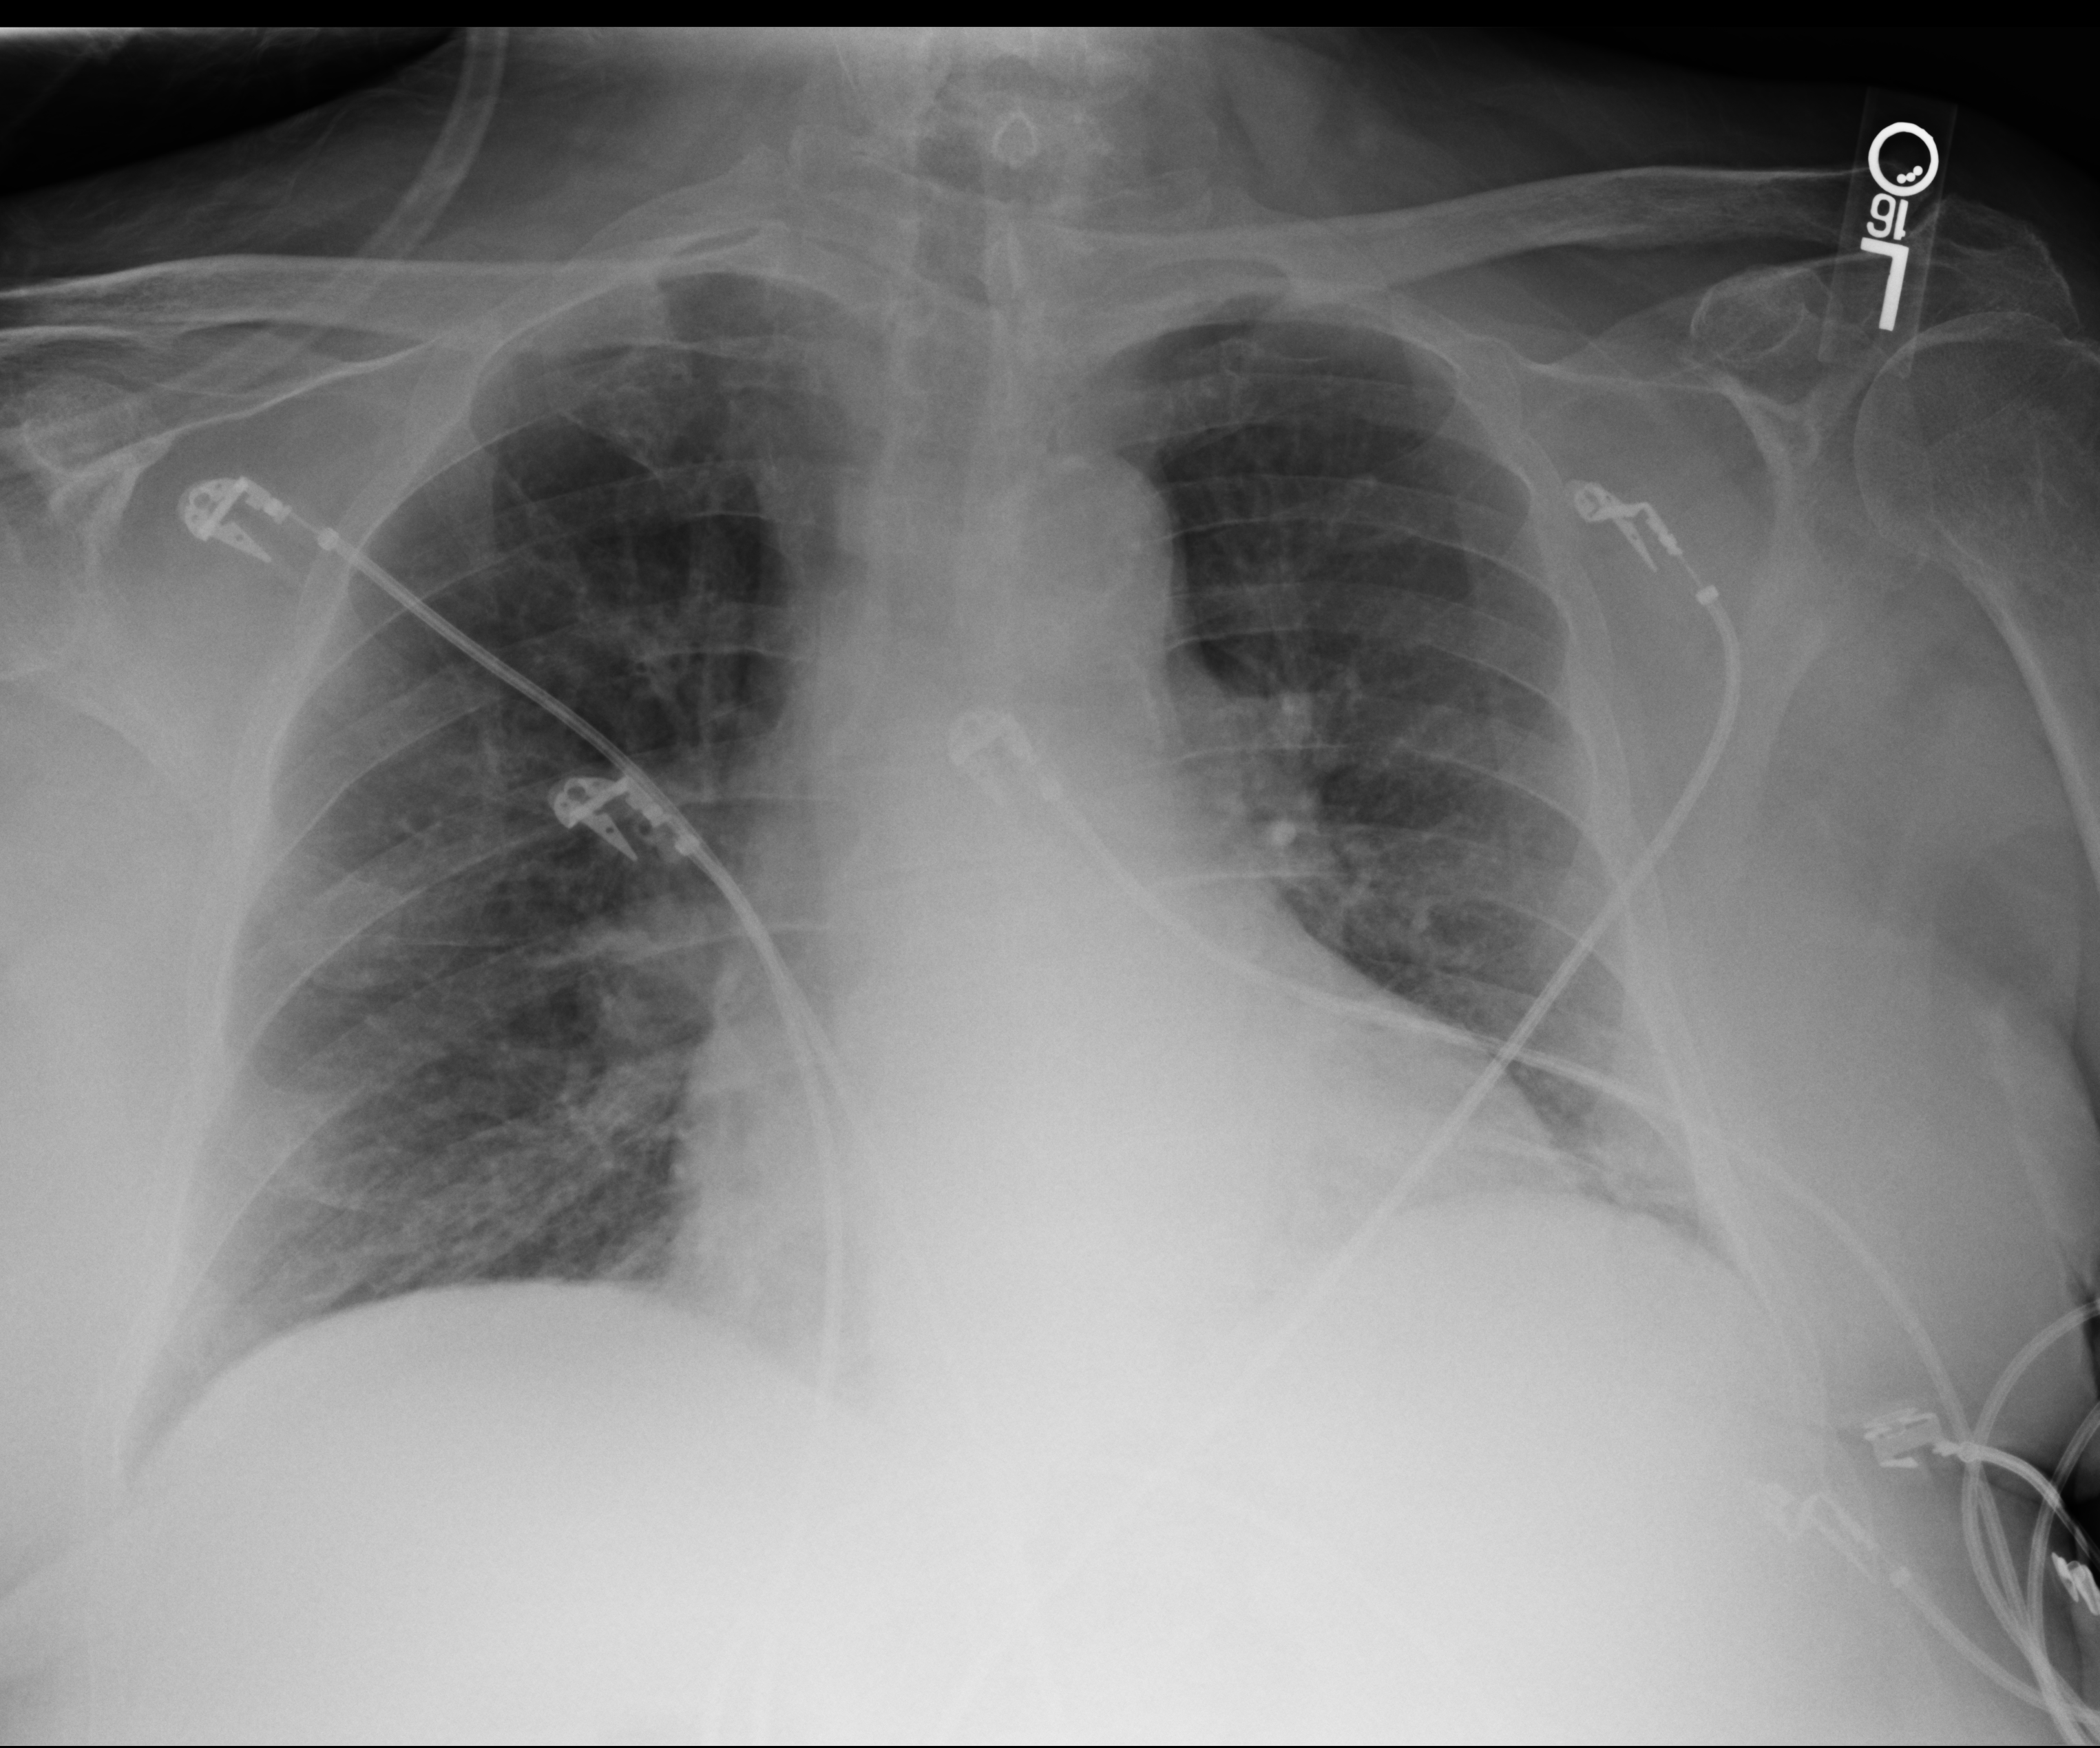
Chest X-ray (portable); anteroposterior (AP) projection. Male patient hospitalised with COVID-19, age 75–90 years.
From the hospital-stay record, not from the radiograph (when in the stay this image was taken is not recorded):
- mechanically ventilated during this hospital stay: no